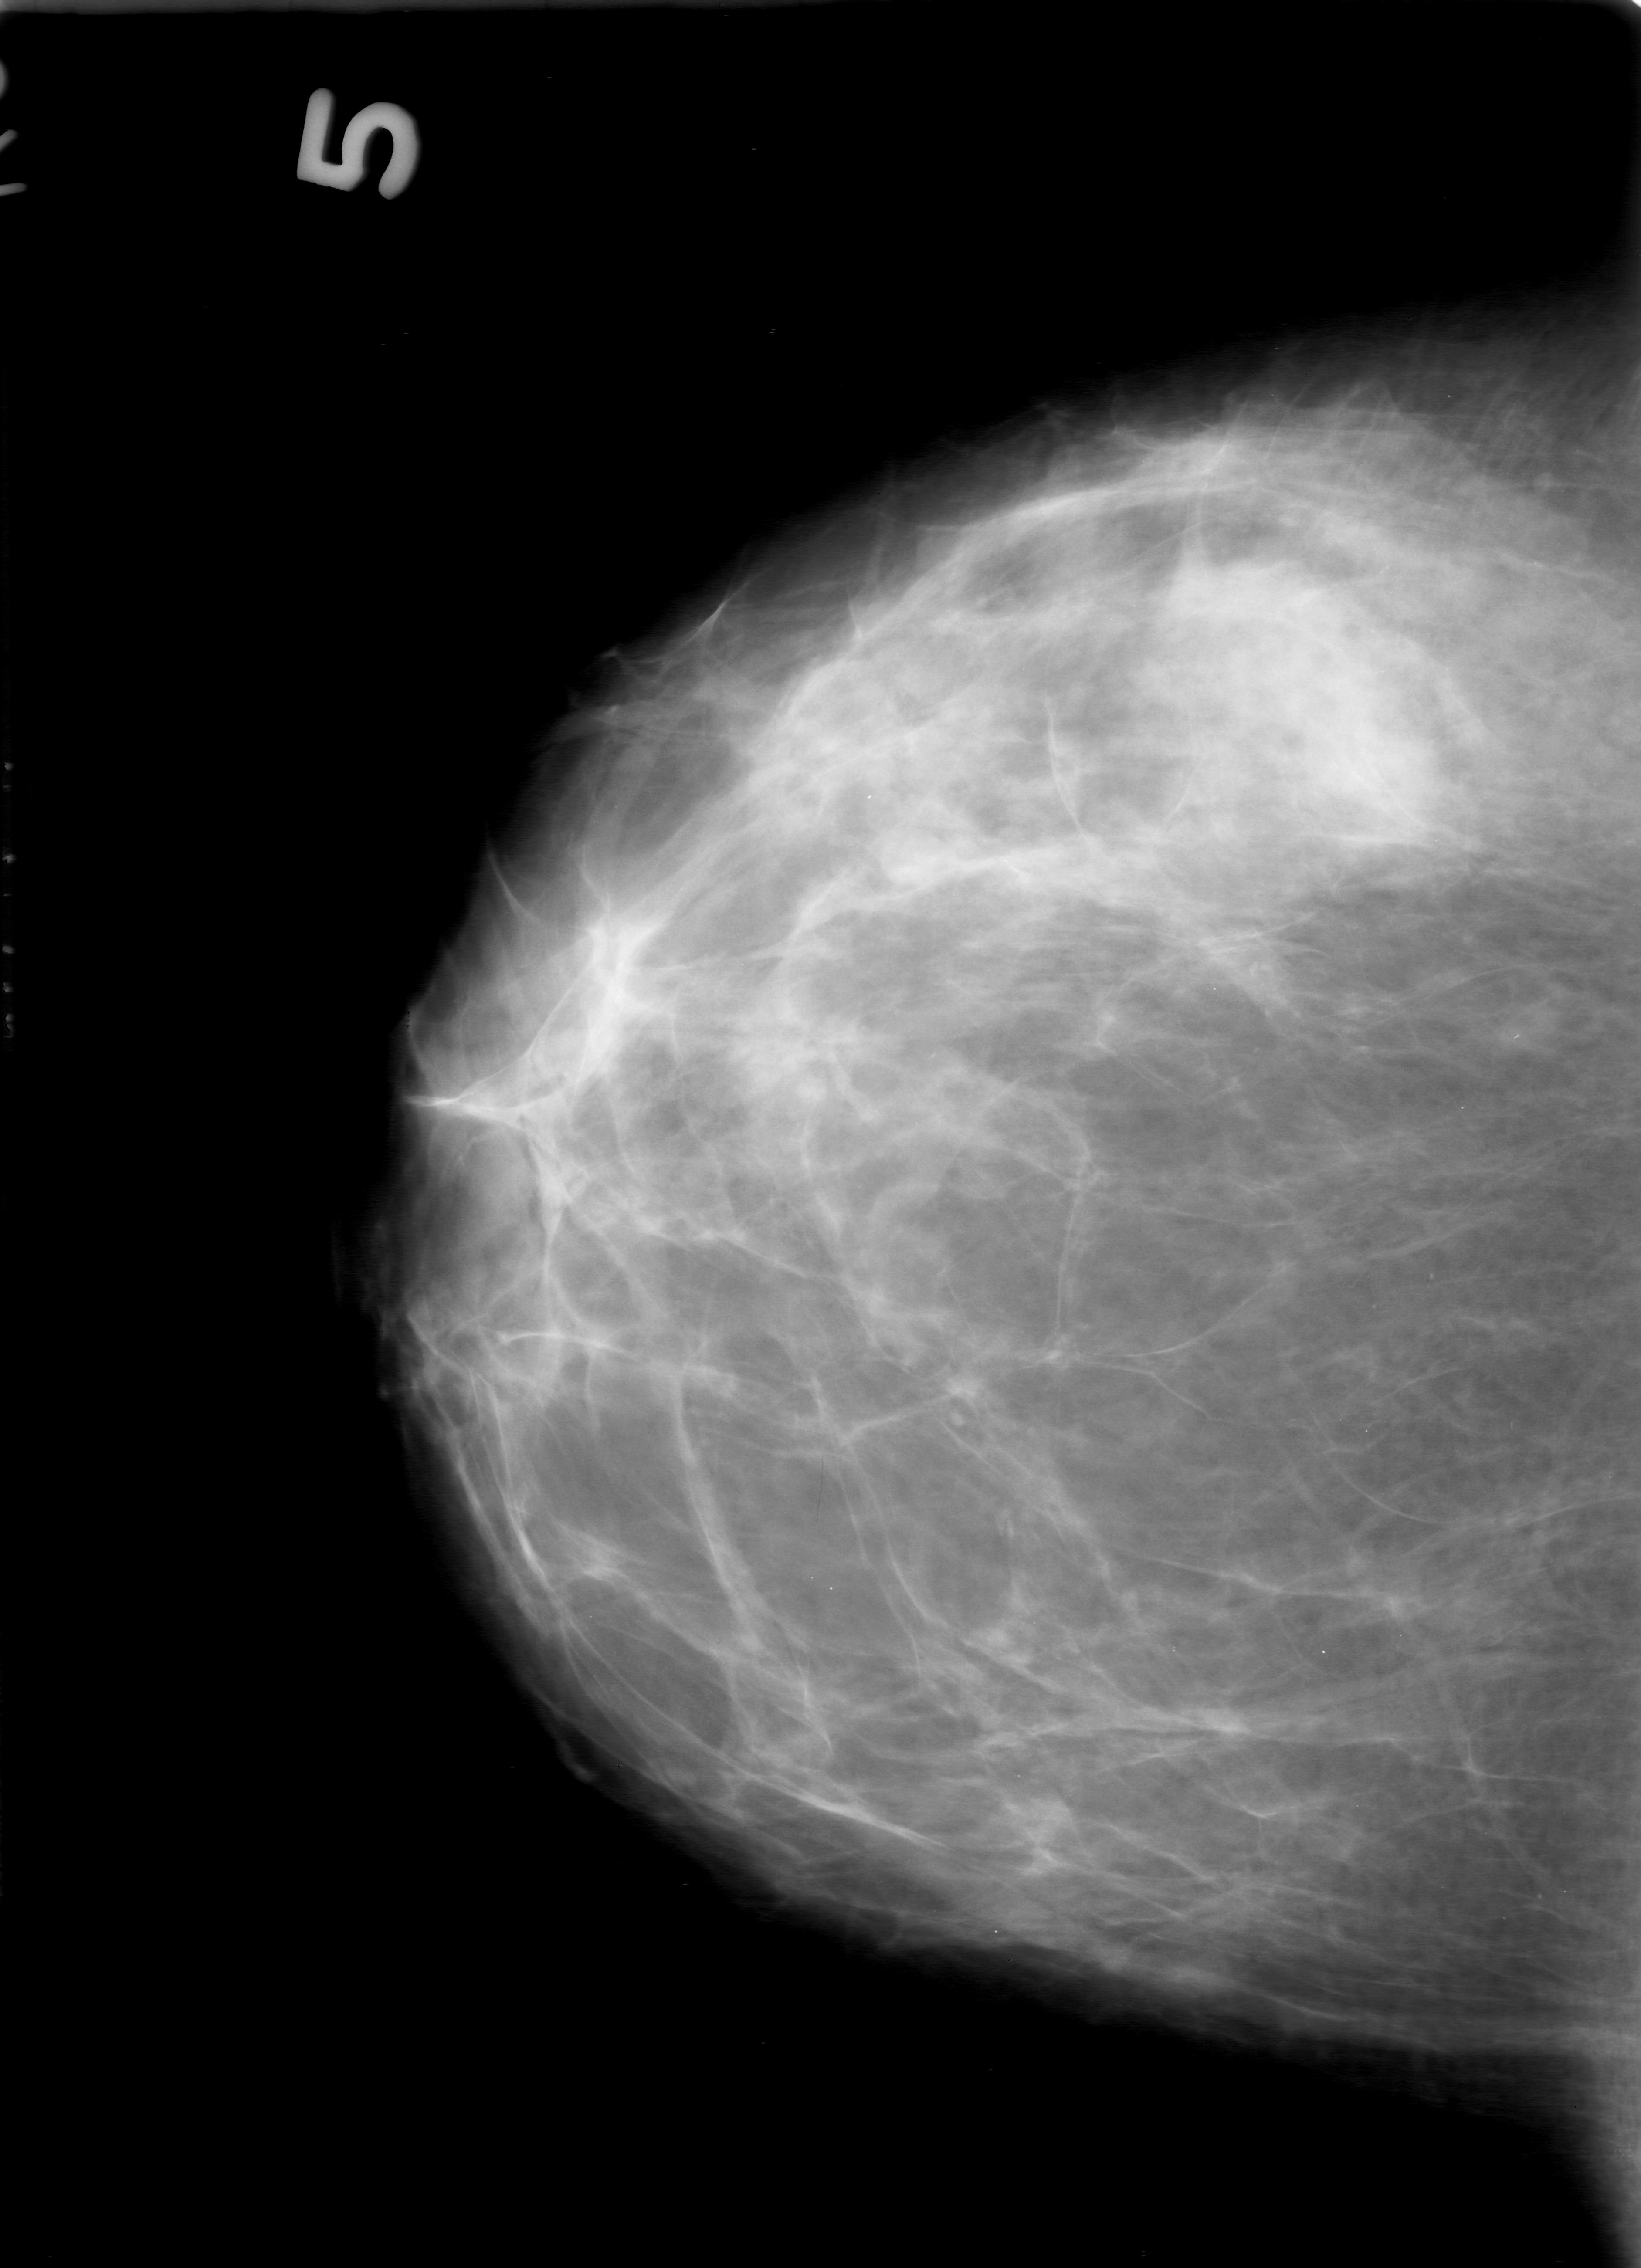
Digitized screen-film mammogram; right breast; CC view; BI-RADS breast density category 3 (scale 1–4); 1641 × 2268 image matrix.
Marked abnormalities (boxes around the expert regions of interest):
- calcifications, morphology punctate / amorphous, distribution clustered; BI-RADS assessment category 0; subtlety rating 2 on a 1 (subtle) to 5 (obvious) scale; pathology result (as recorded, not read from the image): benign: bounding box [x1, y1, x2, y2] px = [1257, 491, 1482, 729]